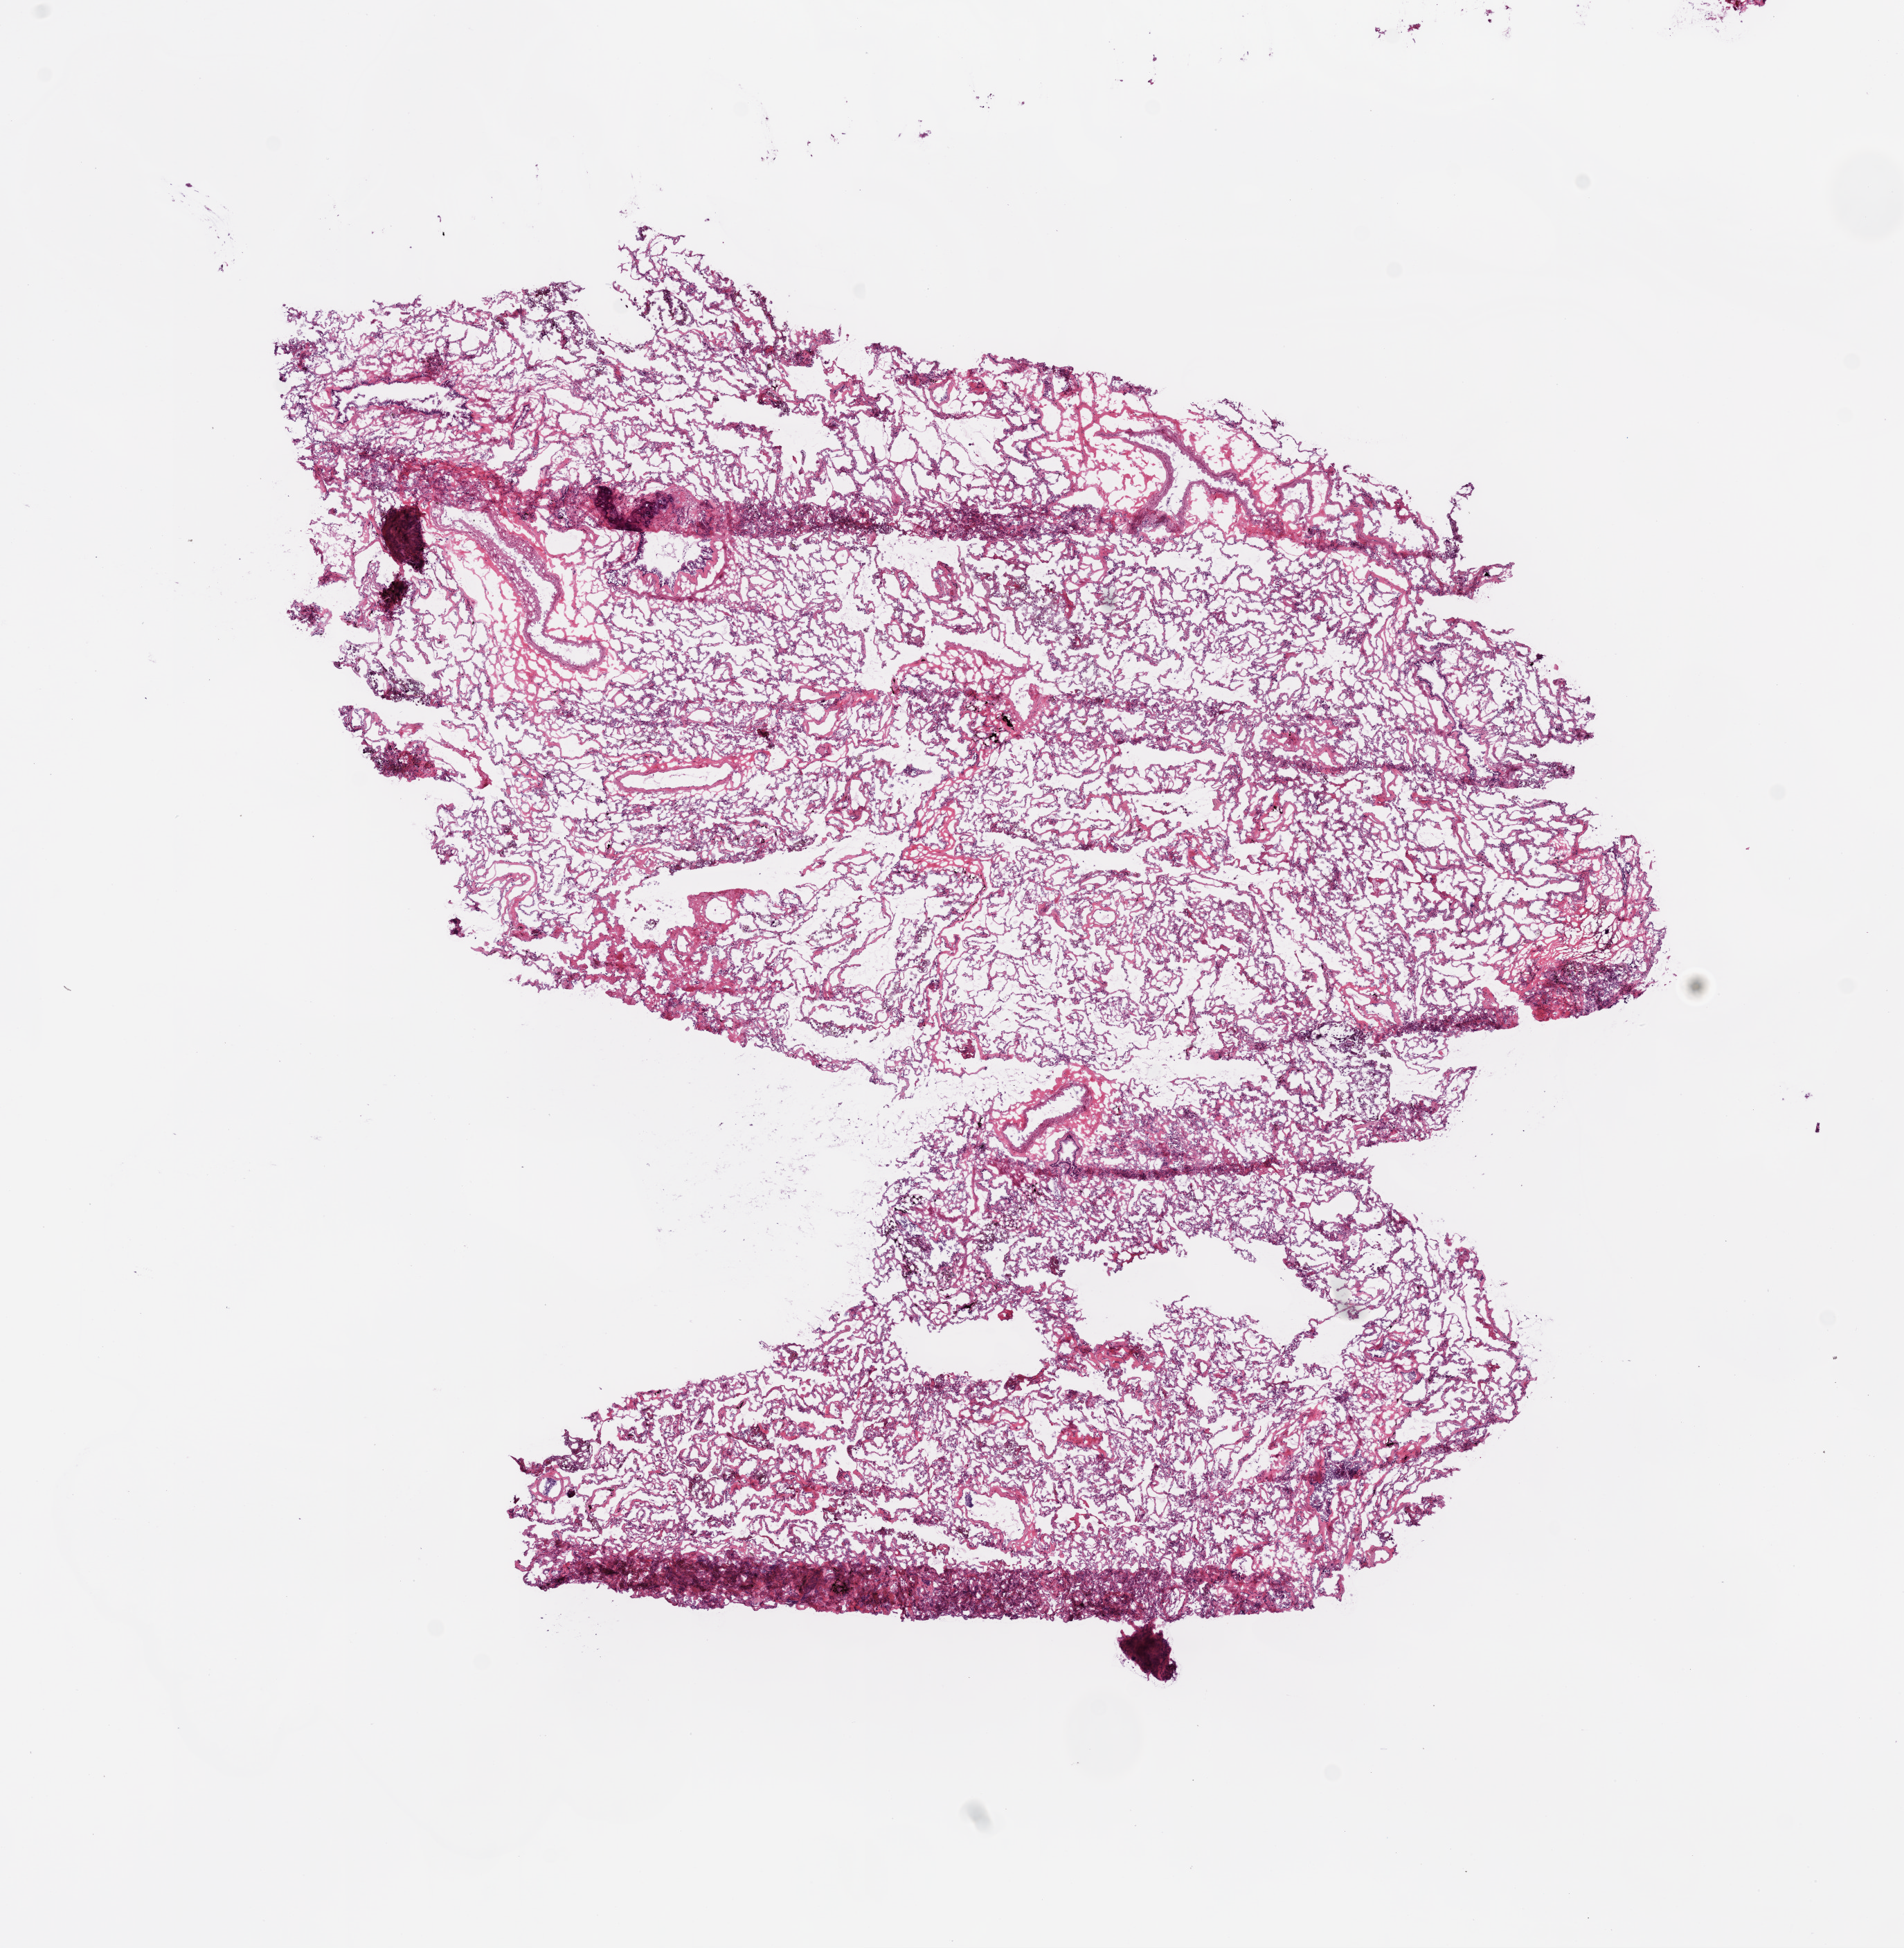
Whole-slide histology image, H&E-stained, a low-resolution overview of the entire scanned area, about 11.0 x 11.3 mm, frozen section from the bottom of the tissue portion, sample: solid tissue normal (non-tumour tissue), lung. Female, age 59 years at initial diagnosis.
This section: solid tissue normal sample (biorepository sample class). Patient diagnosis: Squamous cell carcinoma, NOS (upper lobe, lung).